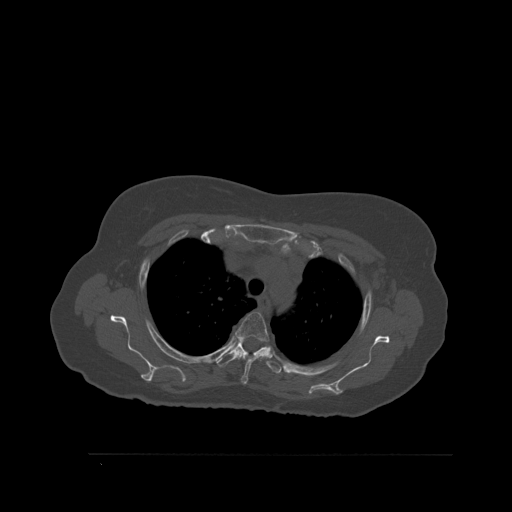
CT including the spine, one axial slice; position 415 of 527 along the scan axis; bone window (W 1800 / L 400 HU); 1.5 mm slice thickness; 512 × 512 image matrix, field of view 470 × 470 mm. Female patient, age 73 years. From the clinical record (not read from this slice): primary cancer: breast.
Structures marked on this image (semi-automatically segmented with operator editing):
- T3 vertebra: box from (x=235, y=312) to (x=270, y=385) px
- T4 vertebra: (x=217, y=338)–(x=282, y=374)